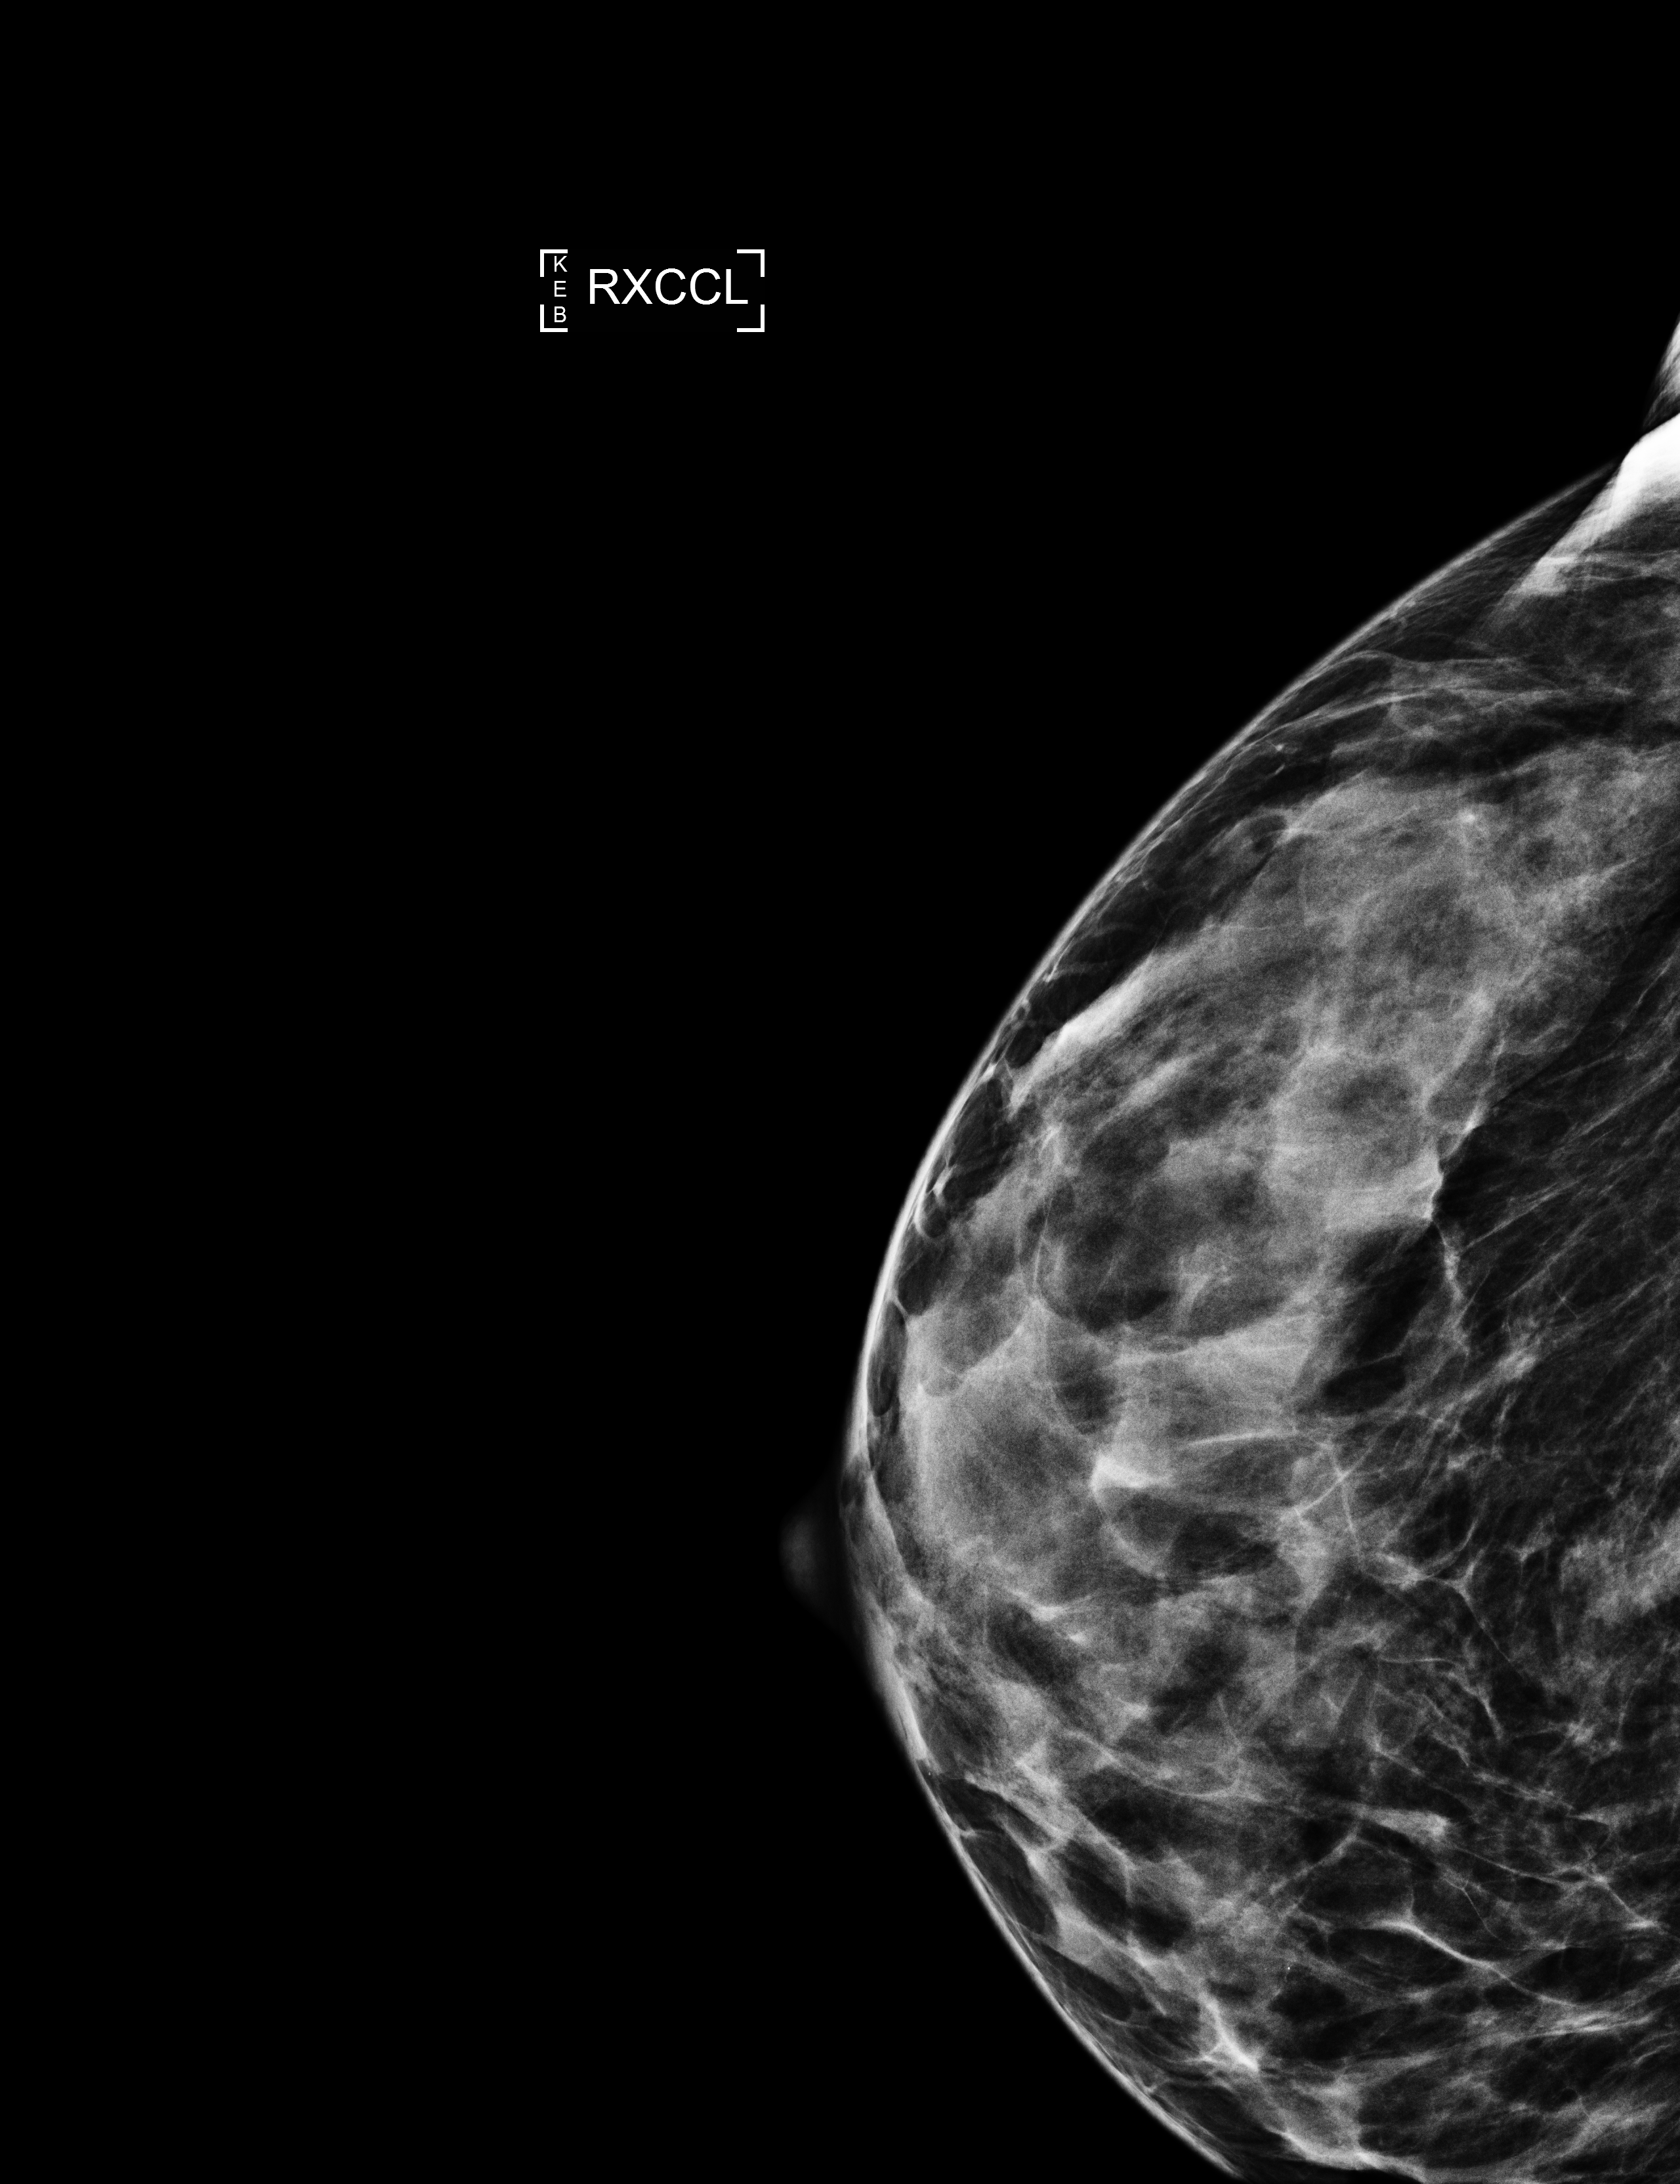
Diagnostic examination (additional views), system: Selenia Dimensions. Patient: female, 56 years.
Image type: full-field digital mammogram. Breast: right. Projection: exaggerated CC view (lateral).